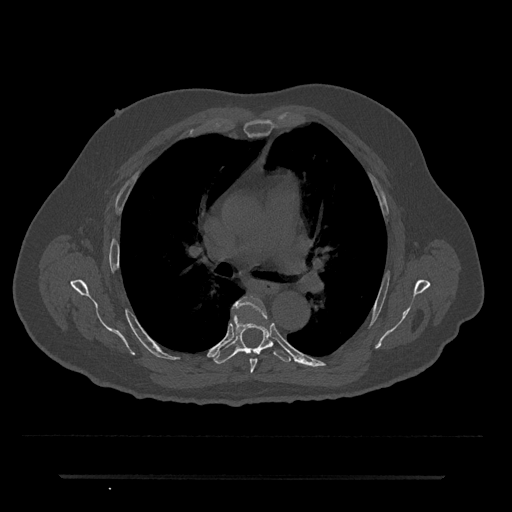
CT including the spine, one axial slice; position 455 of 797 along the scan axis; bone window (W 1800 / L 400 HU); 0.5 mm slice thickness; 512 × 512 image matrix. Patient: male, 69 years. Case-level facts recorded for this patient, not image findings: primary cancer: prostate.
Annotated regions visible in this slice (semi-automatically segmented with operator editing):
- T5 vertebra: bounding box <233,295,267,373> (left, top, right, bottom; pixels)
- T6 vertebra: <214,314,292,364>